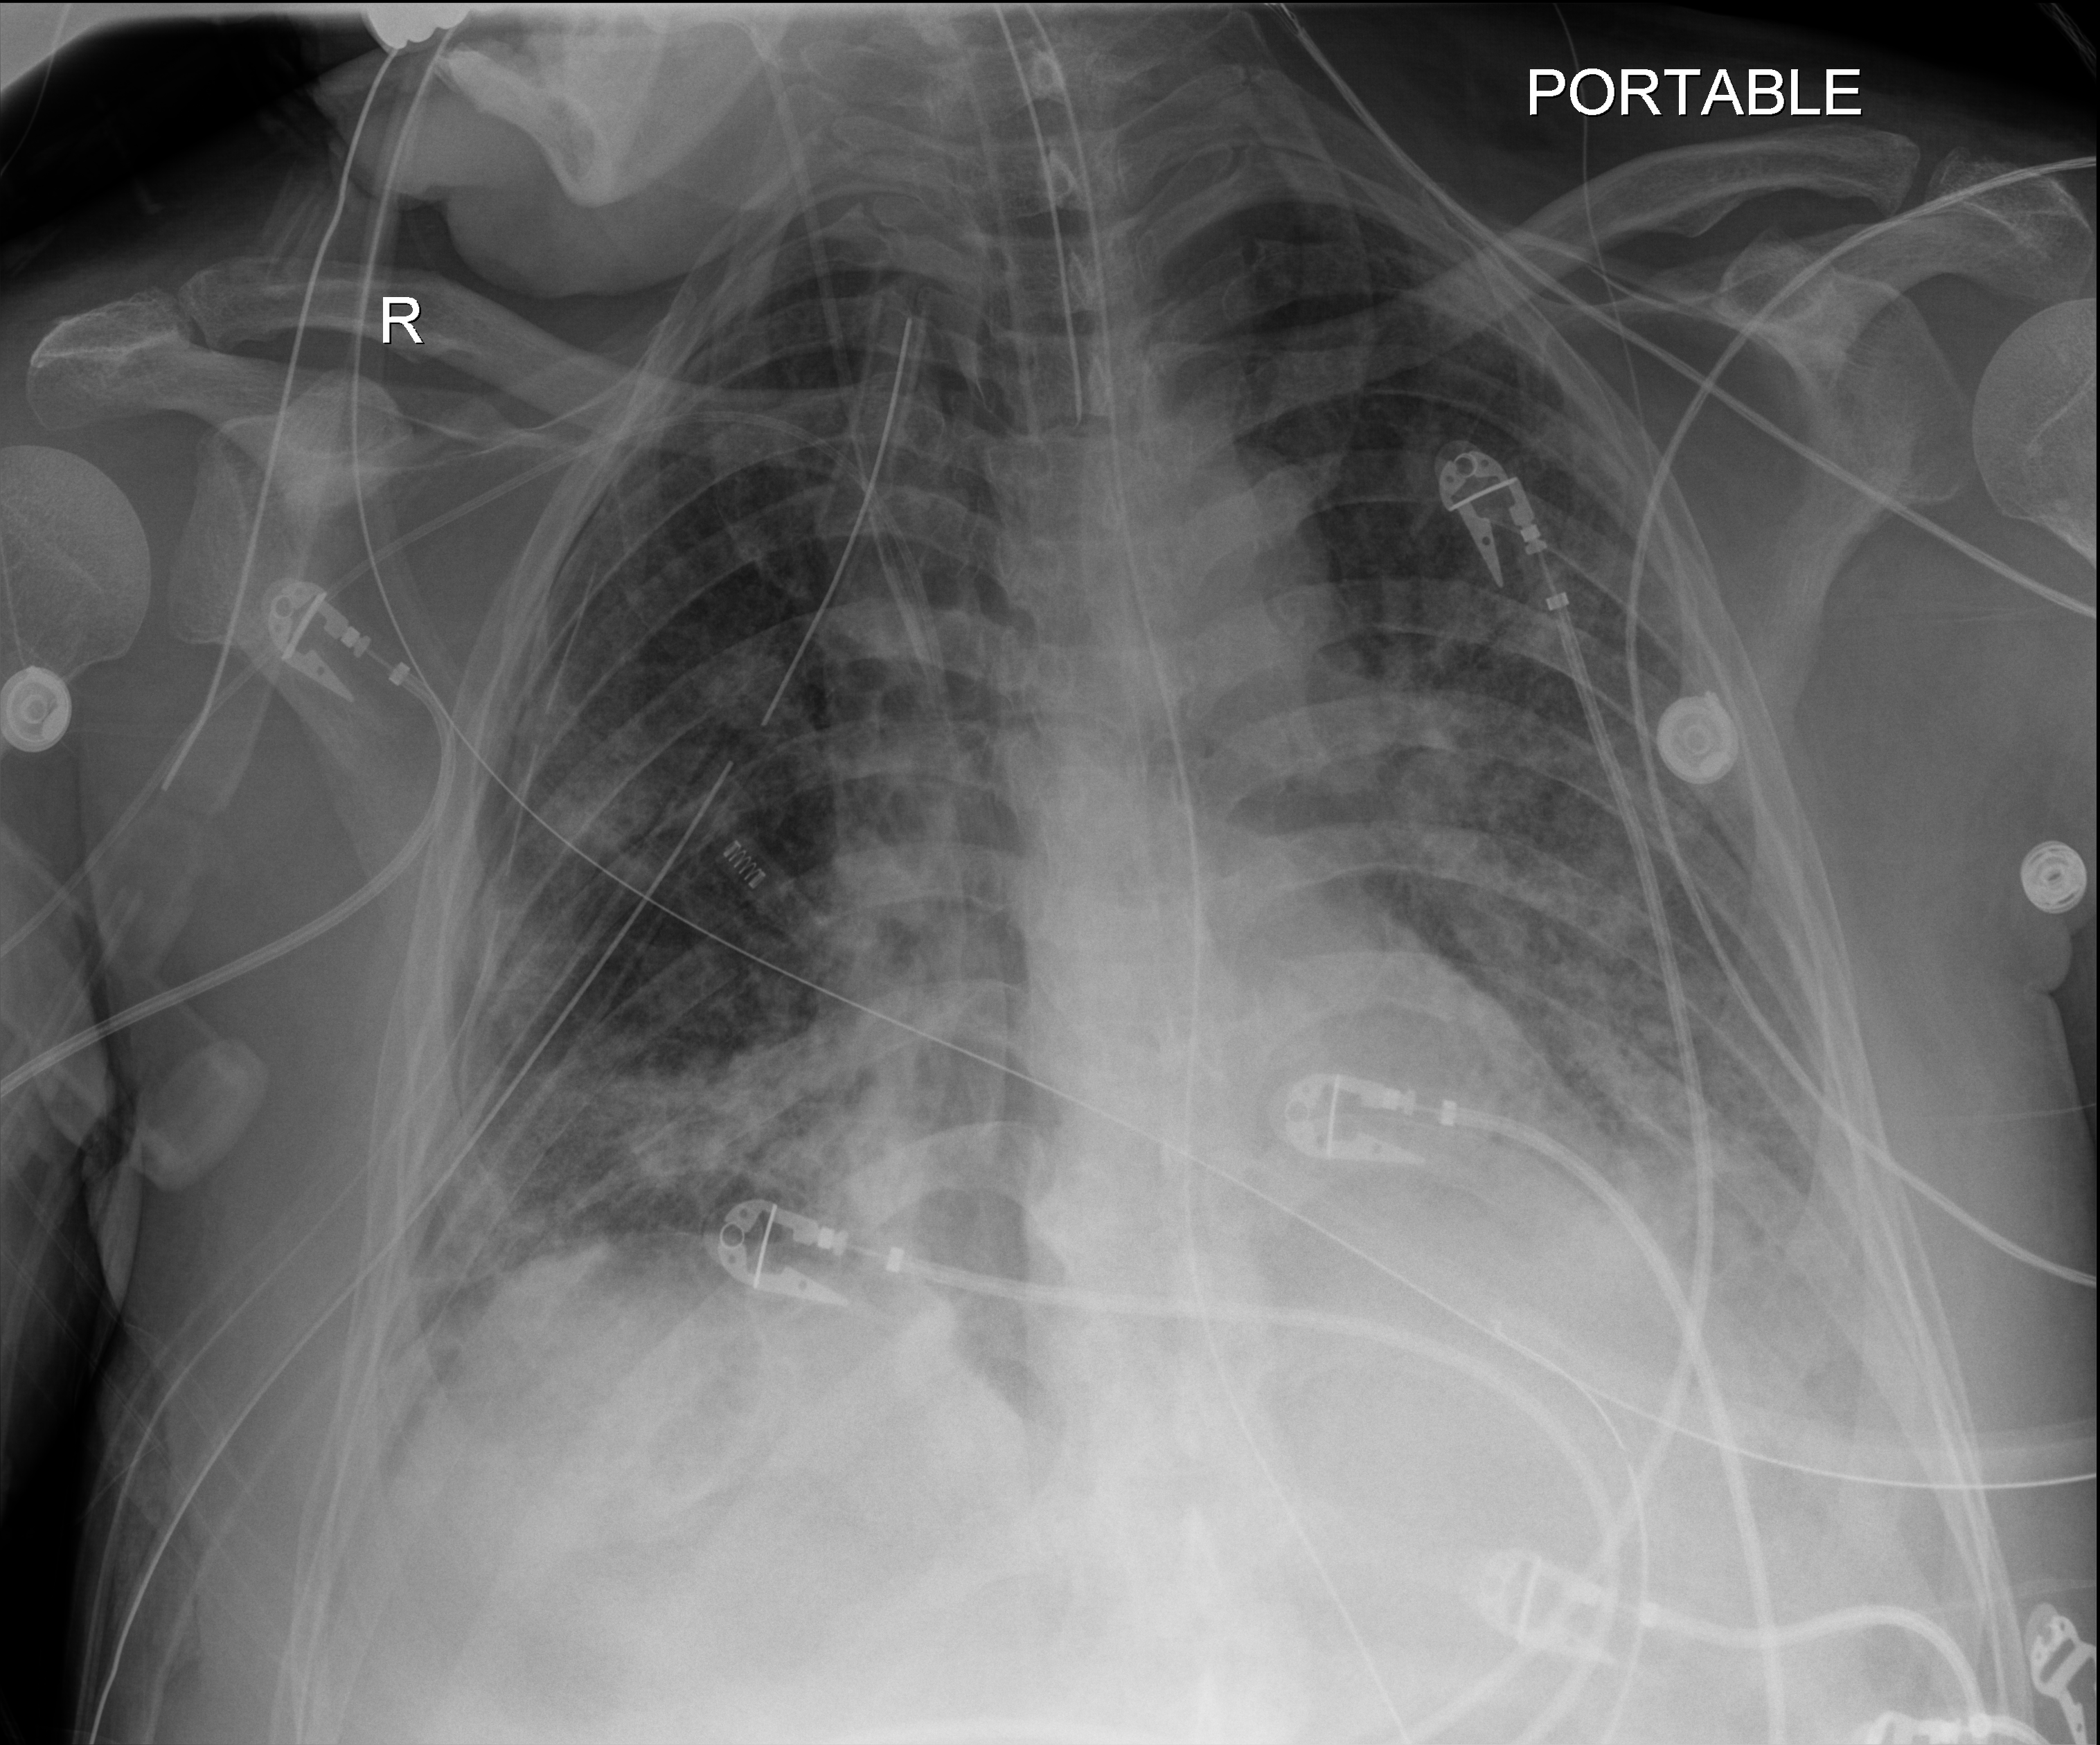
Bedside chest radiograph (digital radiography), anteroposterior (AP) projection. Patient hospitalised with COVID-19; male, aged 60–74 years.
From the hospital-stay record, not from the radiograph (when in the stay this image was taken is not recorded): other chronic lung disease (admission record): no; hypertension (admission record): yes.